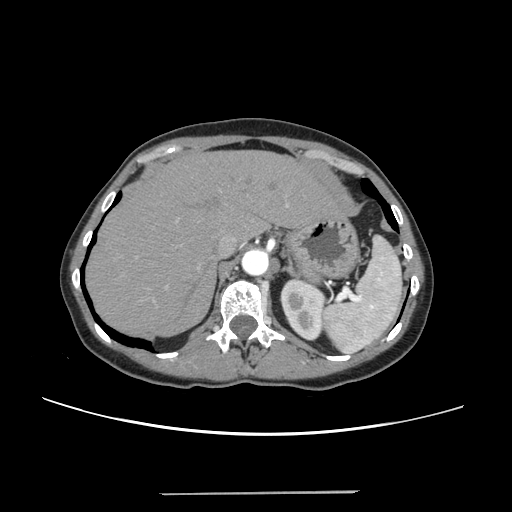
Contrast-enhanced abdominal CT, one axial slice. Slice 185 of 240 in the series (ordered by position). 120 kVp. Intravenous contrast given. Soft-tissue window (W 400 / L 40 HU). 512 × 512 image matrix. Female patient, age 60 years. From the clinical record (not read from this slice): diagnosis: colorectal cancer liver metastases, imaged before liver resection; multiple liver metastases: no; largest metastasis: 1.5 cm; disease in both lobes: no.
Structures marked on this image (expert manual segmentation):
- hepatic veins: bounding box [x1, y1, x2, y2] px = [220, 234, 237, 254]
- liver: [88, 151, 338, 337]
- planned liver remnant (the part of the liver to remain after resection): [88, 151, 338, 337]
- portal vein (with intrahepatic branches): [165, 203, 288, 288]